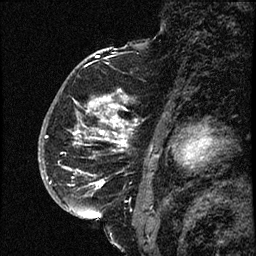
Breast MRI (dynamic contrast-enhanced), one sagittal slice. Position 46 of 66 along the scan axis. Dynamic contrast-enhanced study with each time point stored as its own series, time point 2 of 3 at this slice position (early post-contrast, ordered by acquisition time). 1.5 T. TE 4.2 ms, TR 17.6 ms. 2 mm slice thickness. 256 × 256 image matrix, field of view 200 × 200 mm. Female patient. From the clinical record (not read from this slice): setting: breast cancer imaged before/during neoadjuvant chemotherapy; receptor status: HER2-positive.
Outlined on this slice (semi-automatically segmented with operator editing):
- analysis volume of interest (the breast-tissue region the enhancement analysis was run in; not a lesion): bounding box (x1, y1, x2, y2) in pixels: (52, 69, 142, 209)
- tumour enhancement mask (voxels above the 100 % enhancement threshold inside the analysis volume of interest): (73, 90, 138, 189)